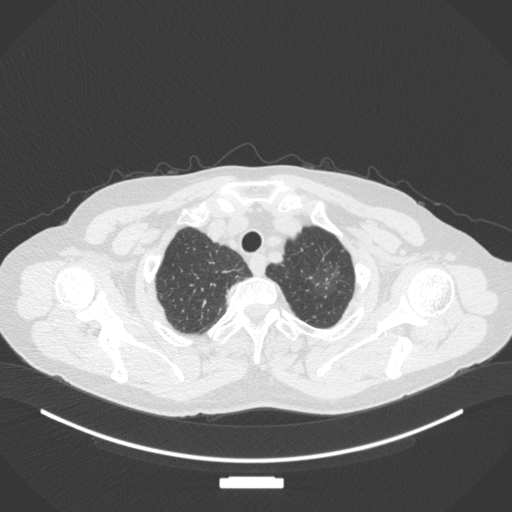
Chest CT, one axial slice. Reconstruction kernel B31f. Lung window (W 1500 / L -600 HU). 512 × 512 image matrix, field of view 400 × 400 mm. Patient: female, 64 years. From the clinical record (not read from this slice): clinical TNM (as recorded): T1c N0 M0; histopathological grade: G1.
Structures marked on this image (rectangle marked by the reading radiologist):
- lung tumour (recorded histology: adenocarcinoma): bounding box [x1, y1, x2, y2] px = [321, 264, 344, 291]